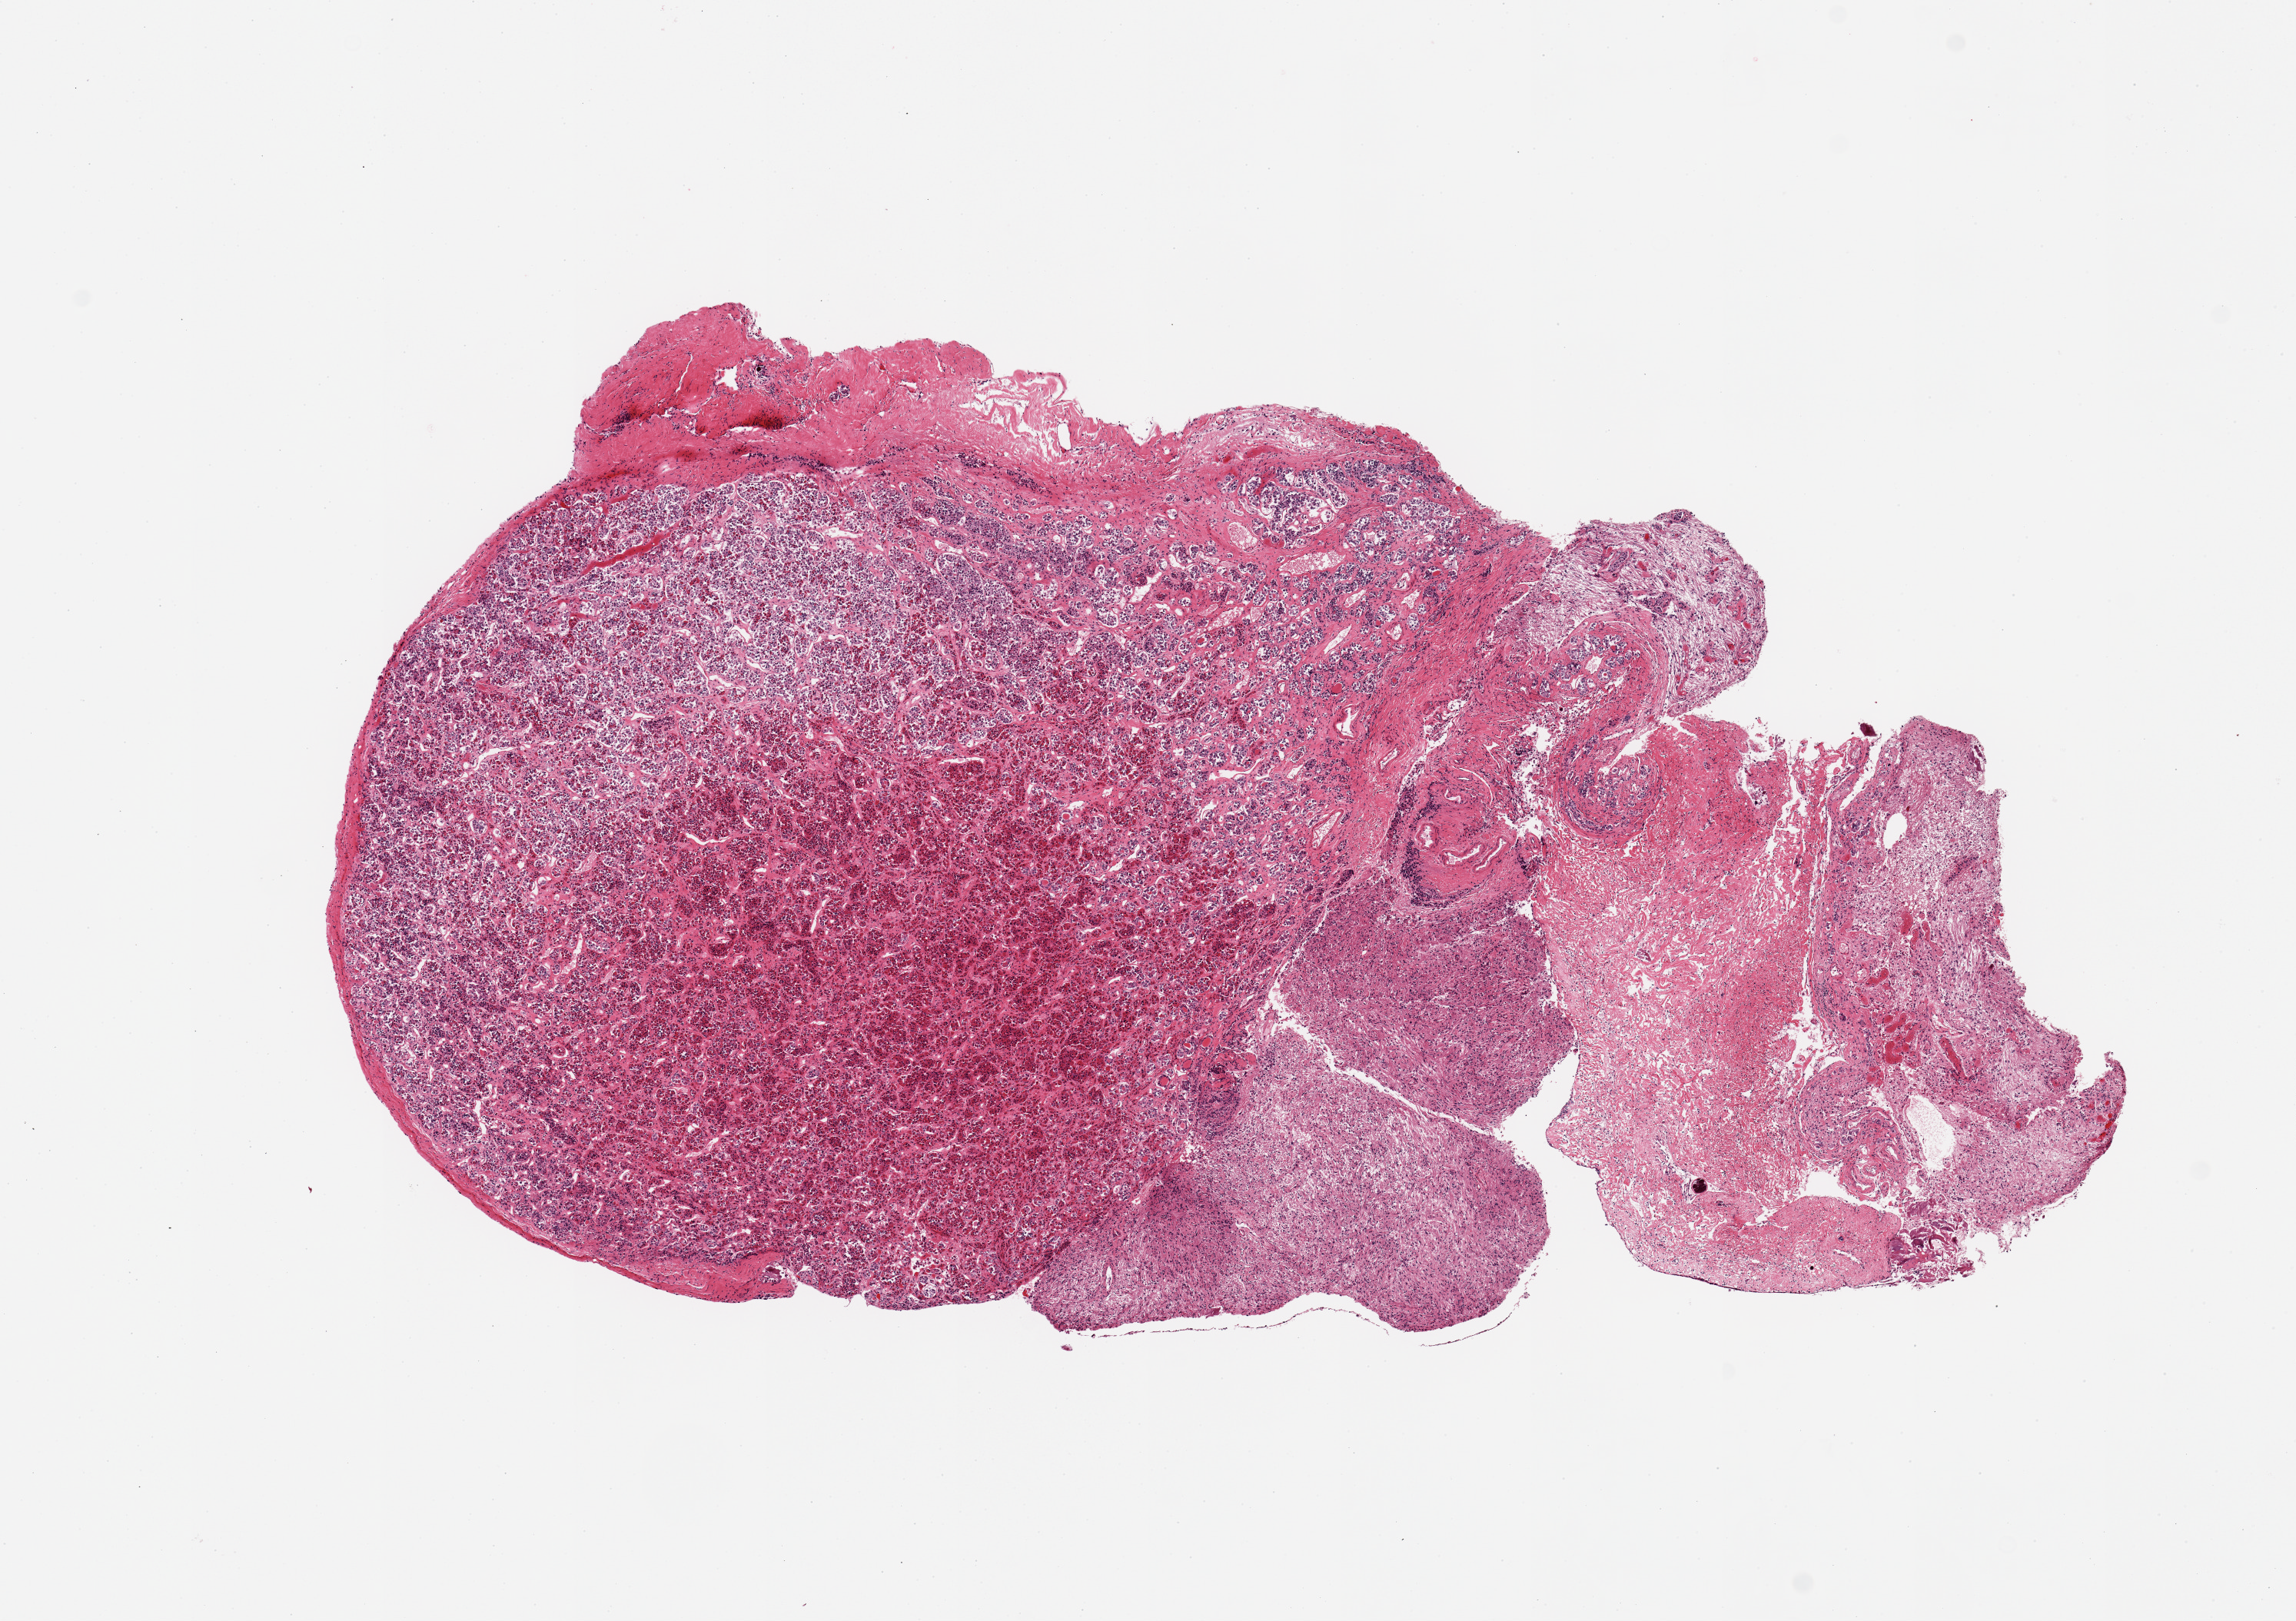
Digitized hematoxylin and eosin (H&E)-stained section — low-resolution overview of the scanned area, about 11.8 x 8.3 mm (slide scanned at 20x); PAXgene-fixed, paraffin-embedded tissue; section of pituitary (target tissue); tissue donor sample. Donor: male.
• reviewer comment on this tissue sample: 1 piece, ~30% neurohypophysis; rest adenohypophysis